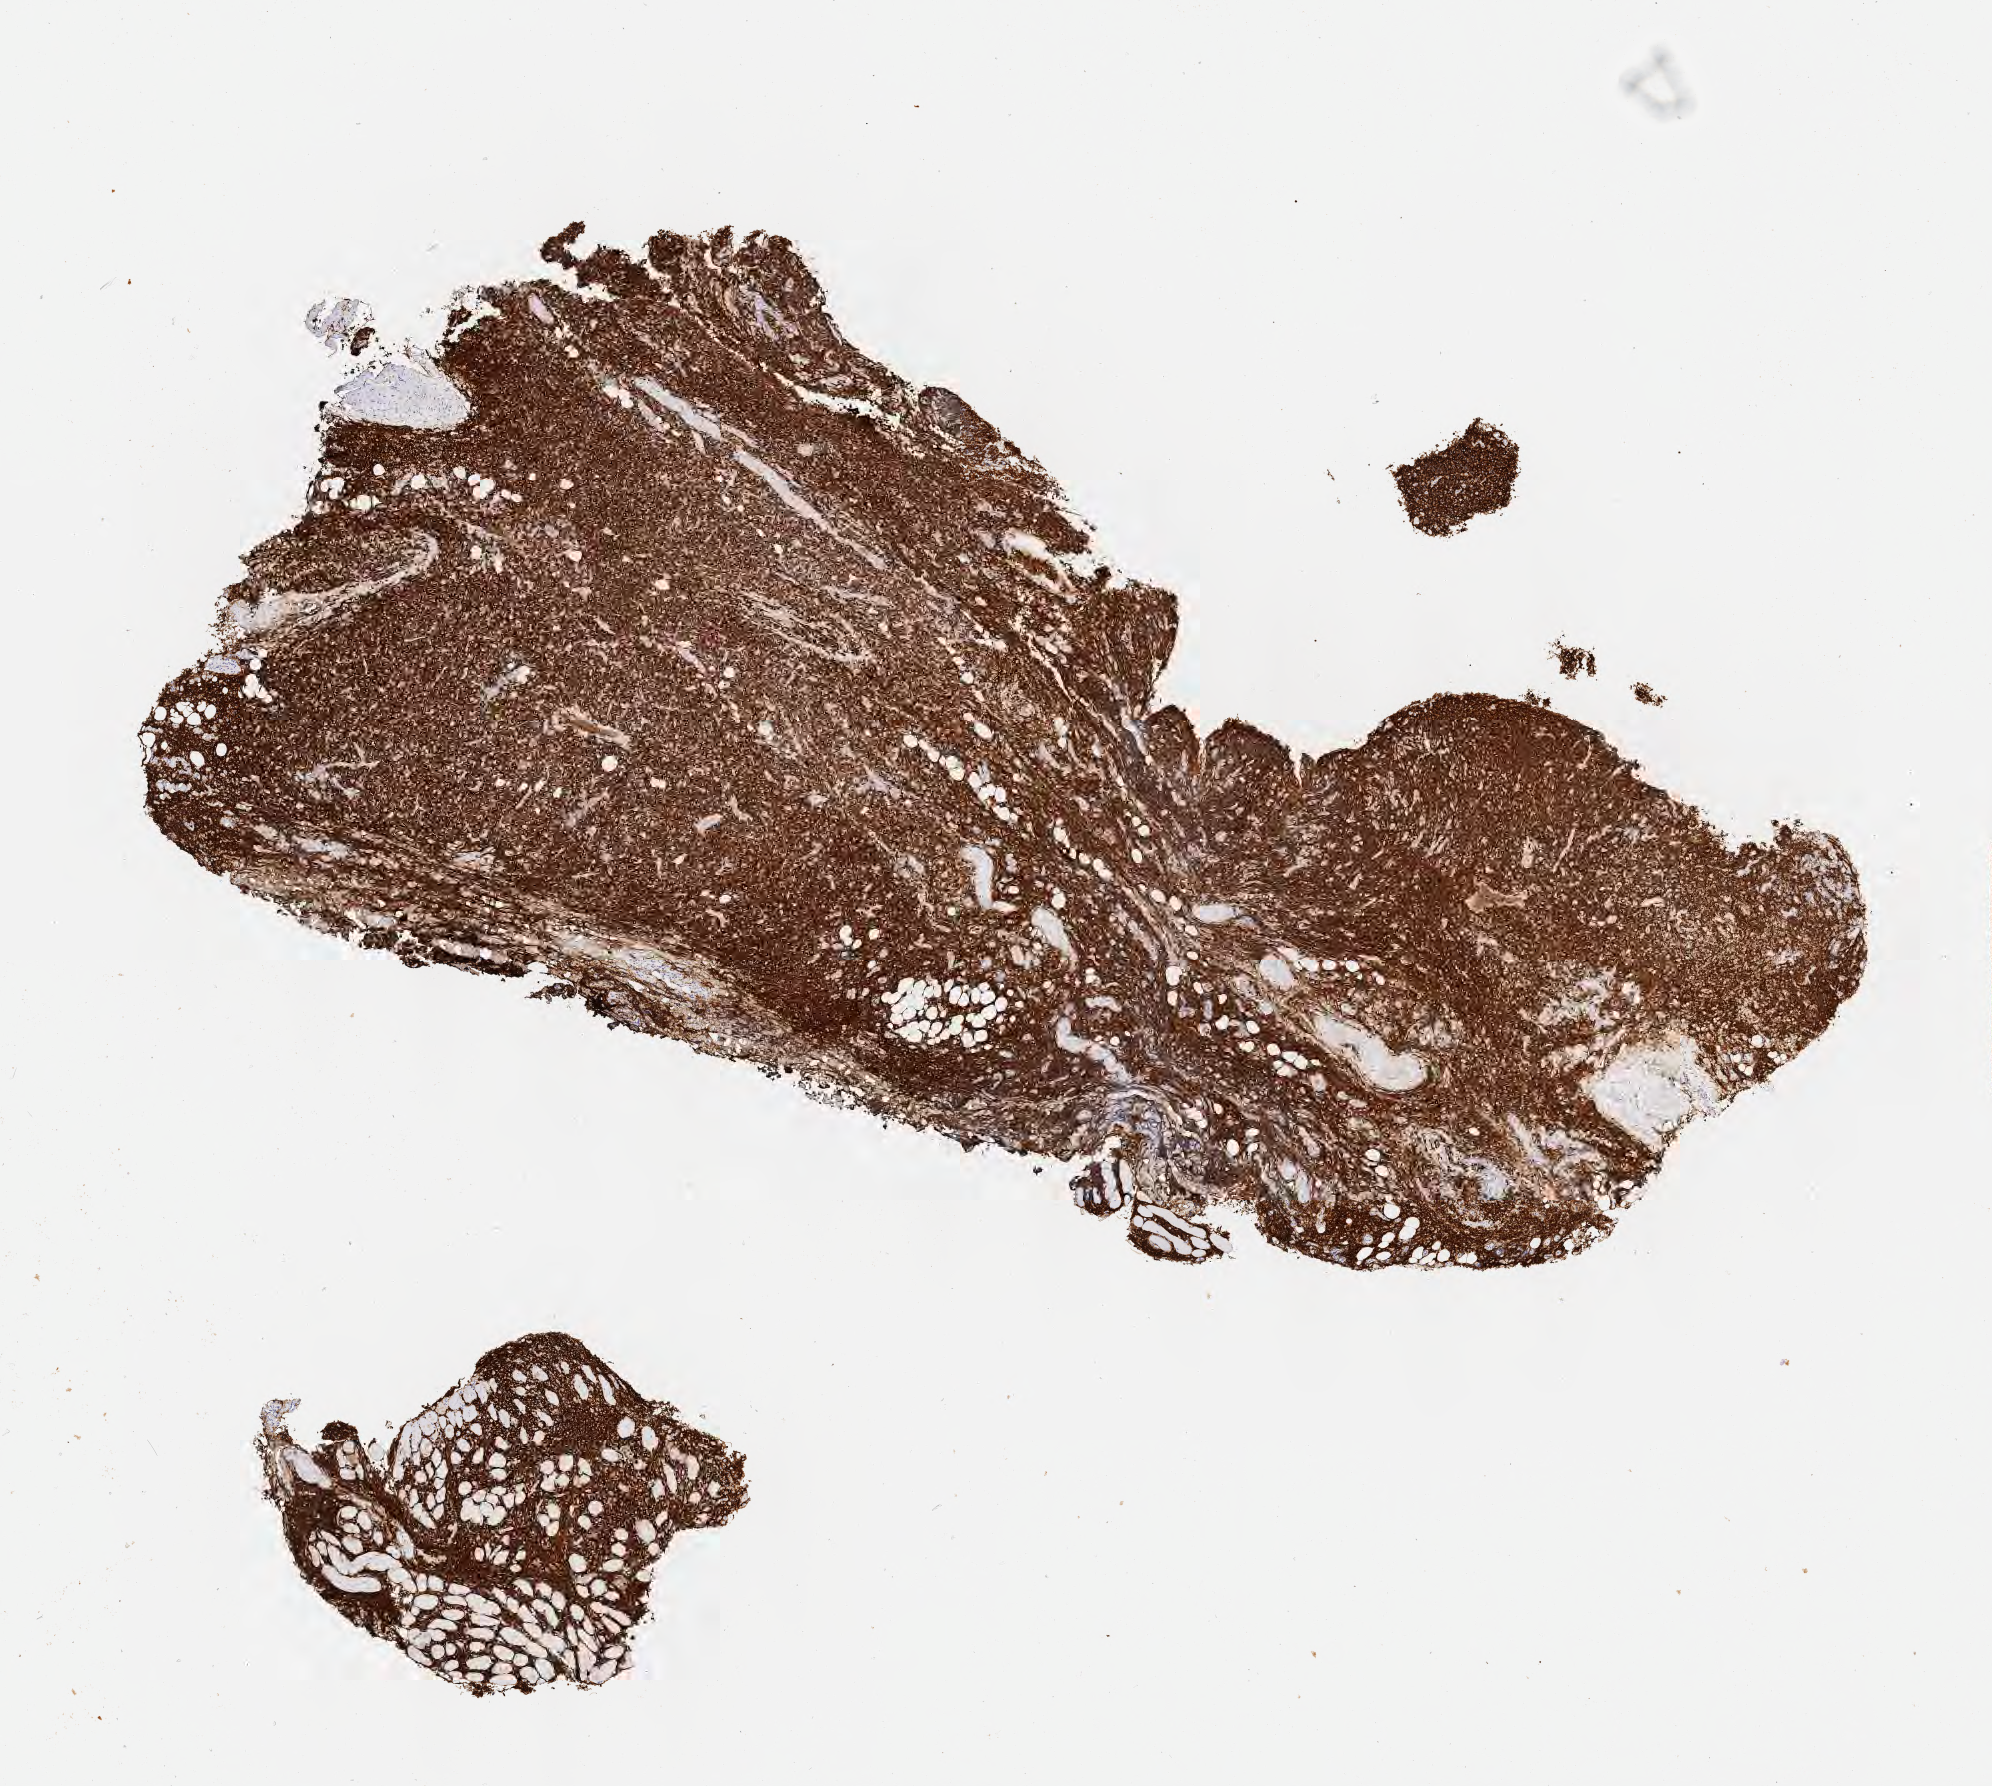
IHC for CD79a, whole-slide image, shown as a low-resolution overview of the whole scanned area (about 8.0 x 7.2 mm), specimen: tumor tissue. Male patient, age 67 years.
* histologic diagnosis: Diffuse large B-cell lymphoma, NOS